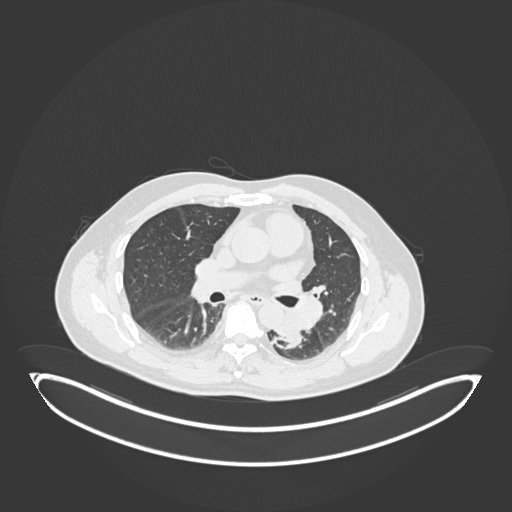
Chest CT, one axial slice; slice 111 of 258 in the series (ordered by position); 120 kVp; lung window (W 1500 / L -600 HU); 512 × 512 image matrix, field of view 500 × 500 mm. Patient: male, 54 years. Case-level facts recorded for this patient, not image findings: clinical TNM (as recorded): T3 N0 M0.
Structures marked on this image (rectangle marked by the reading radiologist):
- lung tumour (recorded histology: squamous cell carcinoma): bounding box [x1, y1, x2, y2] px = [274, 307, 306, 352]